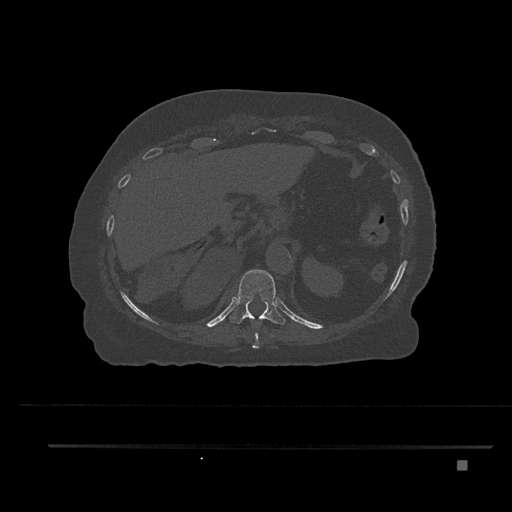
CT including the spine, one axial slice. Slice 319 of 797 in the series (ordered by position). Reconstruction kernel Br40s/3. 120 kVp. Bone window (W 1800 / L 400 HU). 0.5 mm slice thickness. 512 × 512 image matrix, field of view 437 × 437 mm. Patient: female, 76 years. Case-level facts recorded for this patient, not image findings: primary cancer: lung.
Annotated regions visible in this slice (semi-automatically segmented with operator editing):
- T10 vertebra: box from (x=252, y=319) to (x=260, y=348) px
- T11 vertebra: (x=230, y=269)–(x=286, y=325)